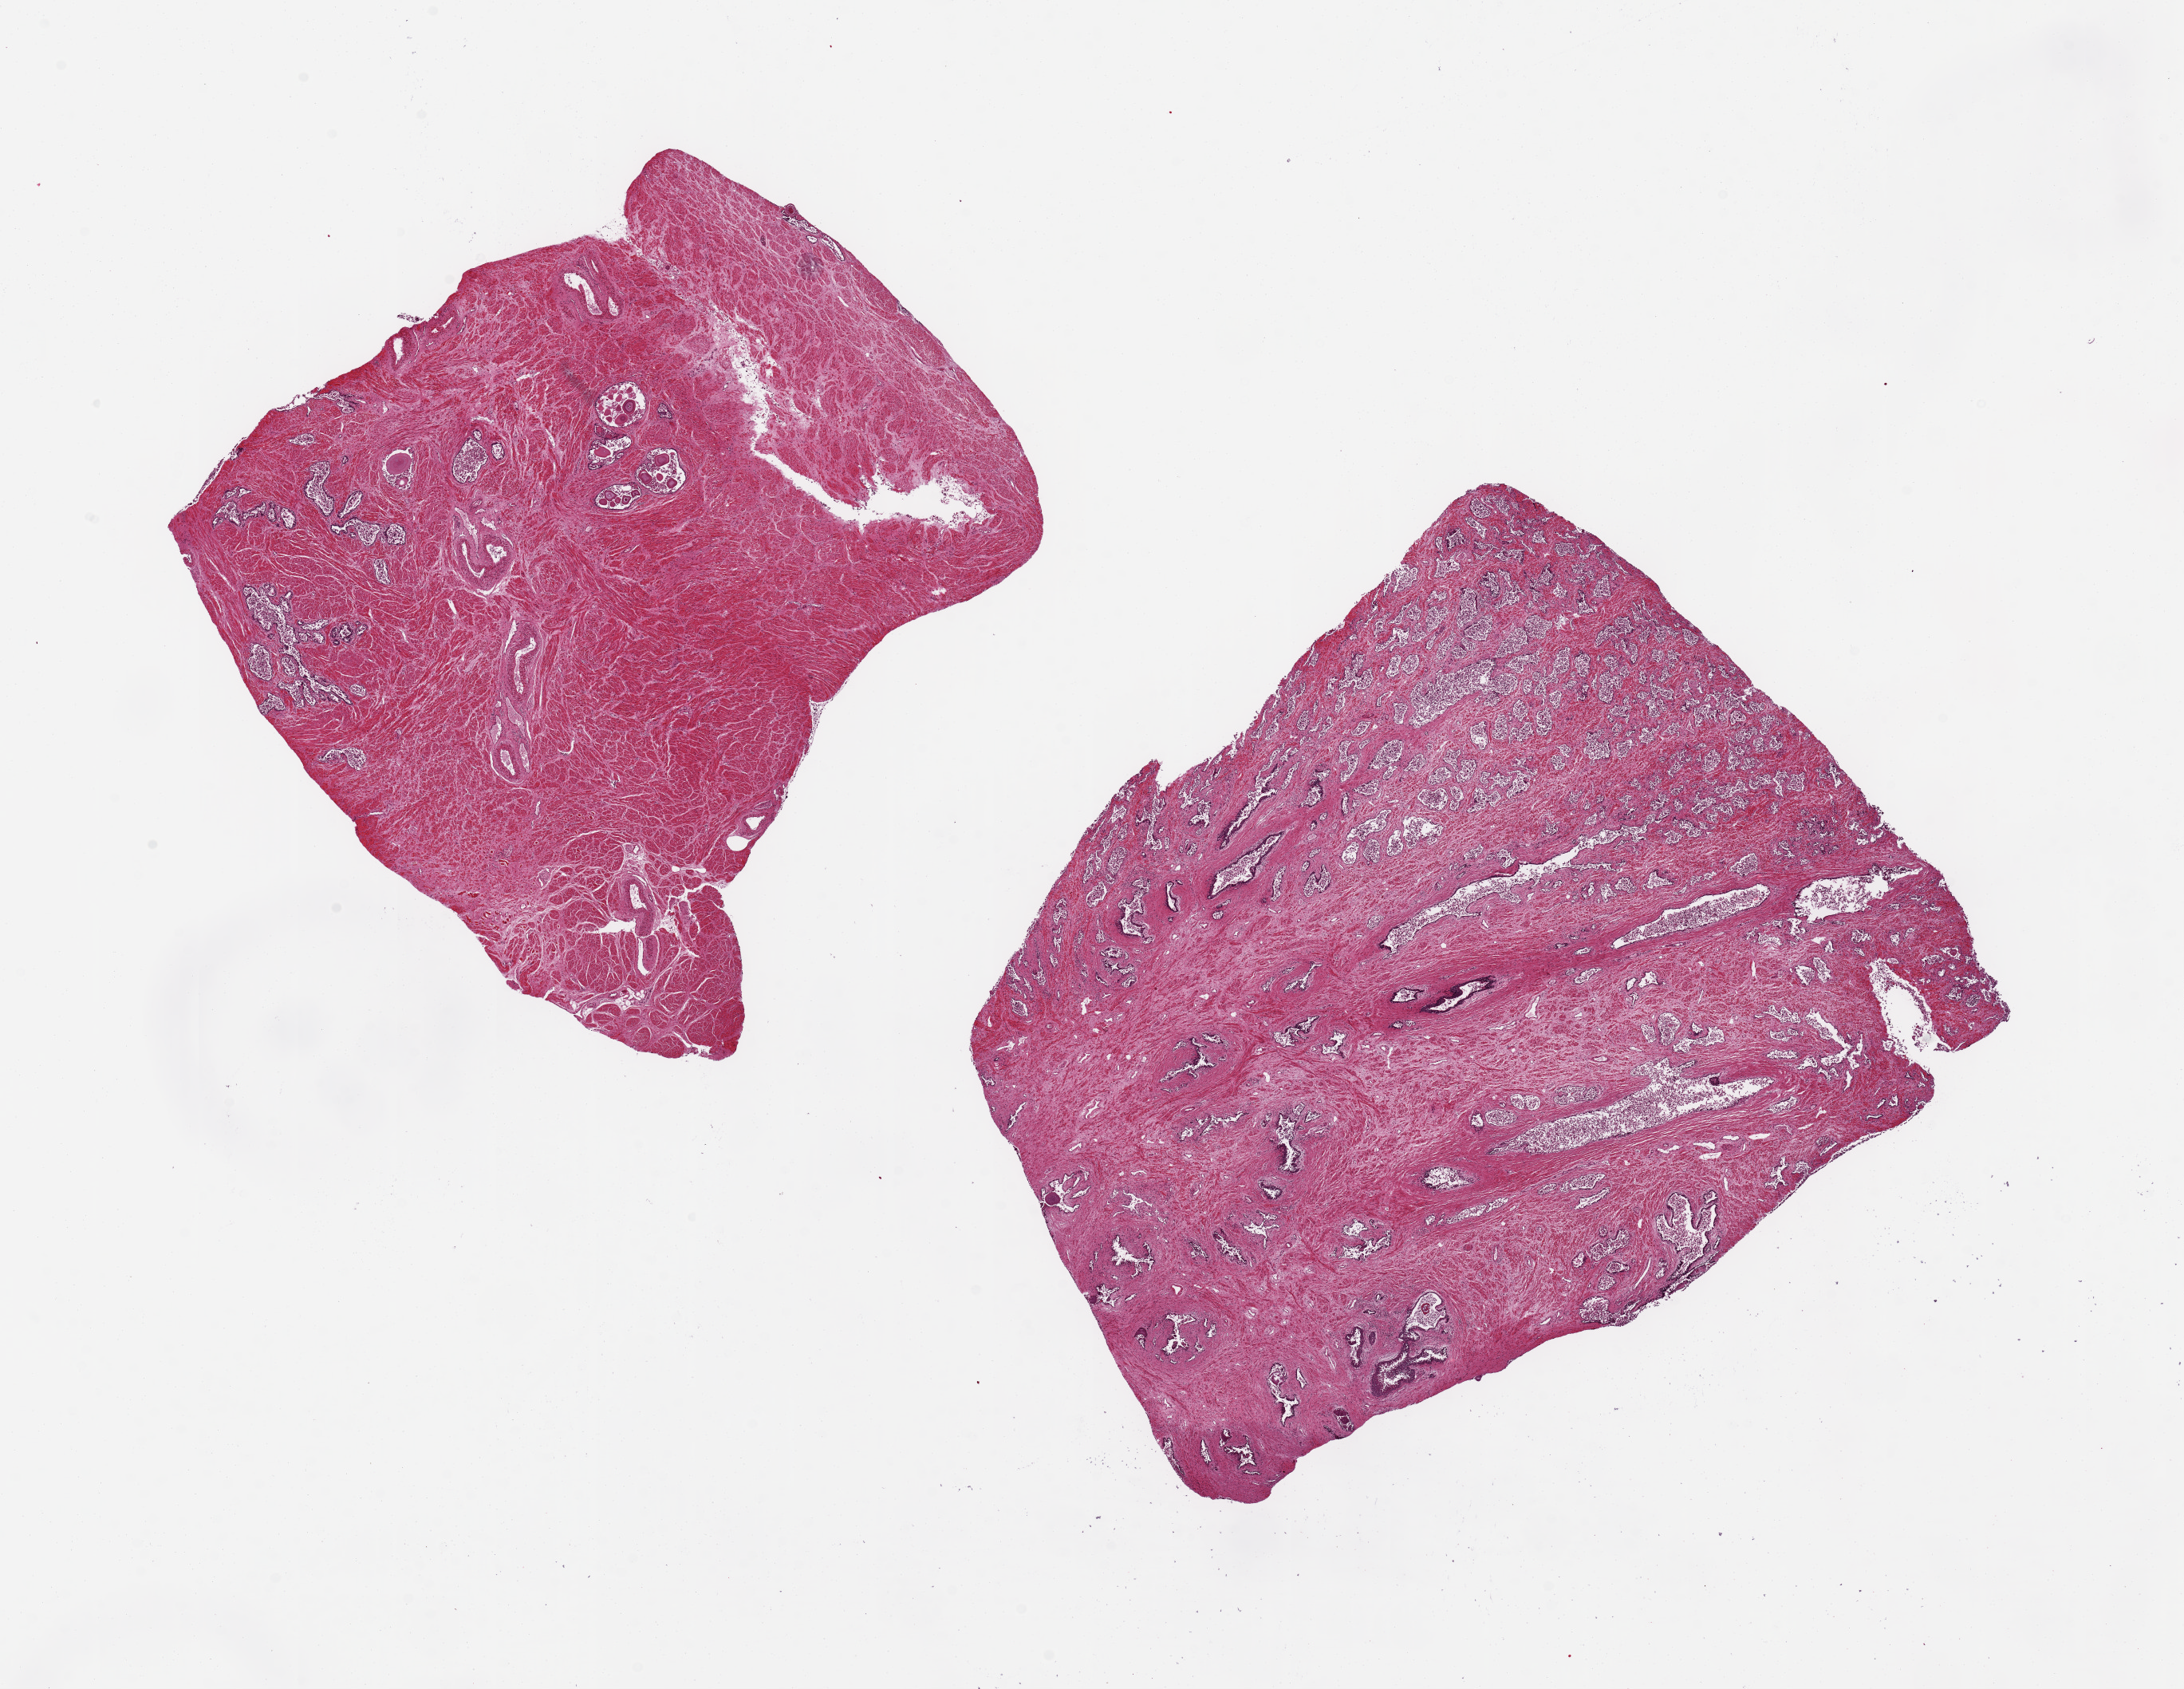
Hematoxylin and eosin (H&E) whole-slide image, shown as a low-resolution overview of the whole scanned area (about 21.7 x 16.7 mm); PAXgene-fixed, paraffin-embedded tissue; target tissue: prostate; tissue donor sample. Donor sex: male.
- review note (as recorded): 2 pieces 9x8 & 8x7 mm; glands autolyzed (3), stroma preserved (1)